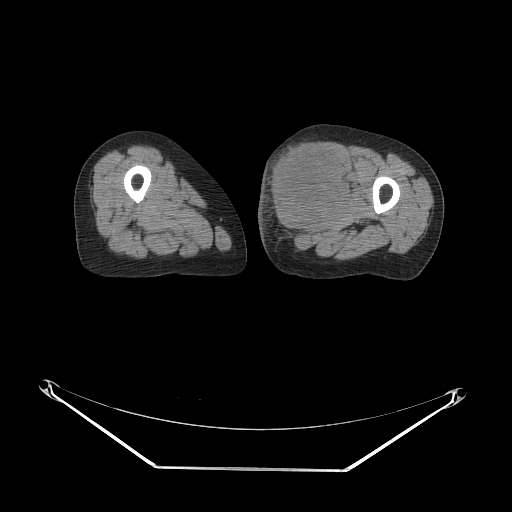
CT of an extremity soft-tissue mass (from a PET/CT study), one axial slice. Slice 37 of 91 in the series (ordered by position). 140 kVp. Soft-tissue window (W 400 / L 40 HU). 3.75 mm slice thickness. 512 × 512 image matrix. Female patient. From the clinical record (not read from this slice): histological type: pleomorphic leiomyosarcoma; grade: high; site of the primary tumour: left thigh.
Structures marked on this image (expert contour drawn on MRI and transferred to this co-registered scan by the dataset authors):
- gross tumour volume including surrounding oedema: box from (x=265, y=139) to (x=353, y=236) px
- gross tumour volume (mass): (x=265, y=139)–(x=348, y=234)